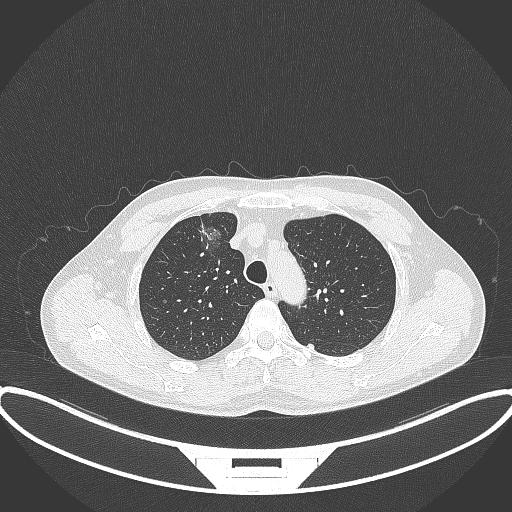
Chest CT, one axial slice; position 283 of 395 along the scan axis; reconstruction kernel B70f; 120 kVp; lung window (W 1500 / L -600 HU); 1 mm slice thickness; 512 × 512 image matrix, field of view 424 × 424 mm. Male patient, age 60 years. From the clinical record (not read from this slice): clinical TNM (as recorded): T1c N0 M0.
Outlined on this slice (rectangle marked by the reading radiologist):
- lung tumour (recorded histology: adenocarcinoma): bounding box <194,213,230,258> (left, top, right, bottom; pixels)